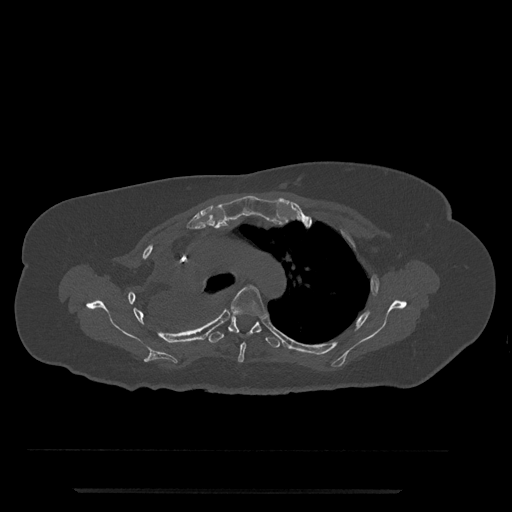
CT including the spine, one axial slice; position 567 of 797 along the scan axis; reconstruction kernel Br40s/3; bone window (W 1800 / L 400 HU); 0.5 mm slice thickness; 512 × 512 image matrix. Patient: female, 51 years. From the clinical record (not read from this slice): primary cancer: neuro; vertebrae with lytic lesions (as recorded): T8.
Annotated regions visible in this slice (semi-automatically segmented with operator editing):
- T4 vertebra: box from (x=229, y=285) to (x=268, y=363) px
- T5 vertebra: (x=207, y=317)–(x=283, y=348)